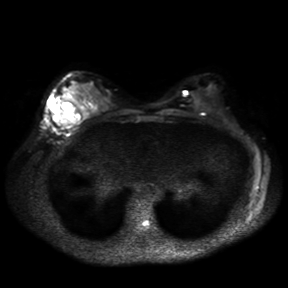
Breast MRI, one axial slice; position 18 of 30 along the scan axis; diffusion-weighted series; image 2 of 4 stored at this slice position (different b-values; order by instance number); 3 T; 4 mm slice thickness; 288 × 288 image matrix, field of view 360 × 360 mm. Female patient.
Annotated regions visible in this slice (outlined manually by an expert reader):
- tumour on diffusion-weighted imaging: box from (x=49, y=99) to (x=68, y=127) px